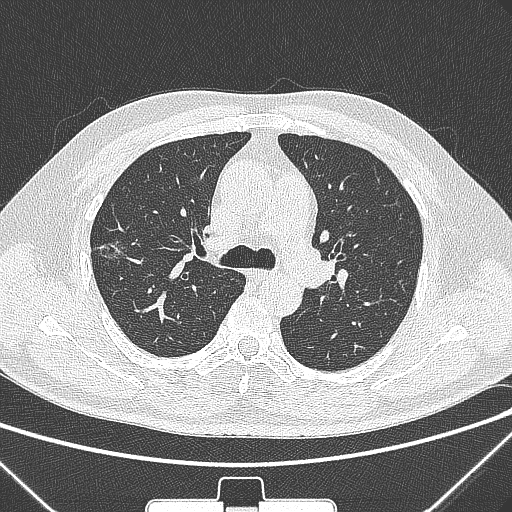
Chest CT, one axial slice. Slice 202 of 320 in the series (ordered by position). Lung window (W 1500 / L -600 HU). 1 mm slice thickness. 512 × 512 image matrix, field of view 350 × 350 mm. Patient: male, 58 years. Case-level facts recorded for this patient, not image findings: clinical TNM (as recorded): T1c N0 M0; histopathological grade: G2.
Annotated regions visible in this slice (bounding box drawn by a radiologist):
- lung tumour (recorded histology: adenocarcinoma): bounding box <95,232,133,272> (left, top, right, bottom; pixels)